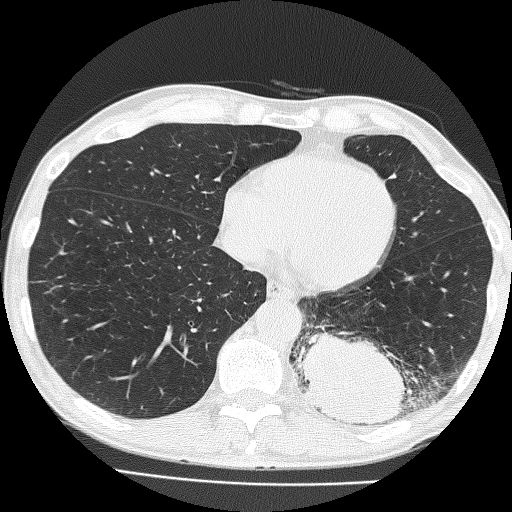
Low-dose screening chest CT, one axial slice. Position 56 of 160 along the scan axis. Reconstruction kernel FC51. 120 kVp. Lung window (W 1500 / L -600 HU). 2 mm slice thickness. 512 × 512 image matrix.
Annotated regions visible in this slice (outlined manually by an expert reader):
- lesion 1 (tumor, lower lobe of left lung): bounding box (x1, y1, x2, y2) in pixels: (294, 331, 409, 426)